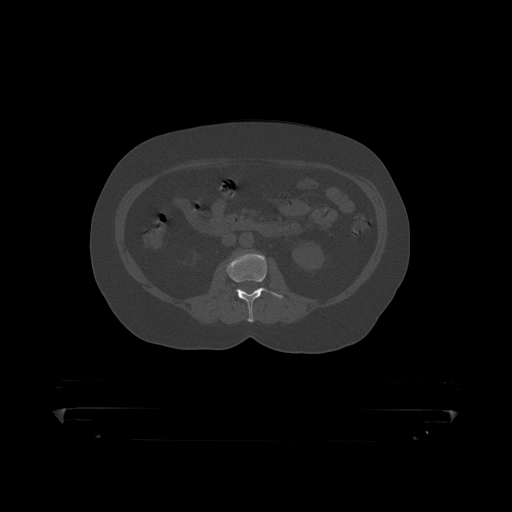
CT including the spine, one axial slice. Slice 112 of 390 in the series (ordered by position). Reconstruction kernel STANDARD. 120 kVp. Bone window (W 1800 / L 400 HU). 512 × 512 image matrix, field of view 650 × 650 mm. Patient: male, 60 years. From the clinical record (not read from this slice): primary cancer: prostate.
Structures marked on this image (semi-automatically segmented with operator editing):
- L2 vertebra: bounding box (x1, y1, x2, y2) in pixels: (227, 253, 284, 319)